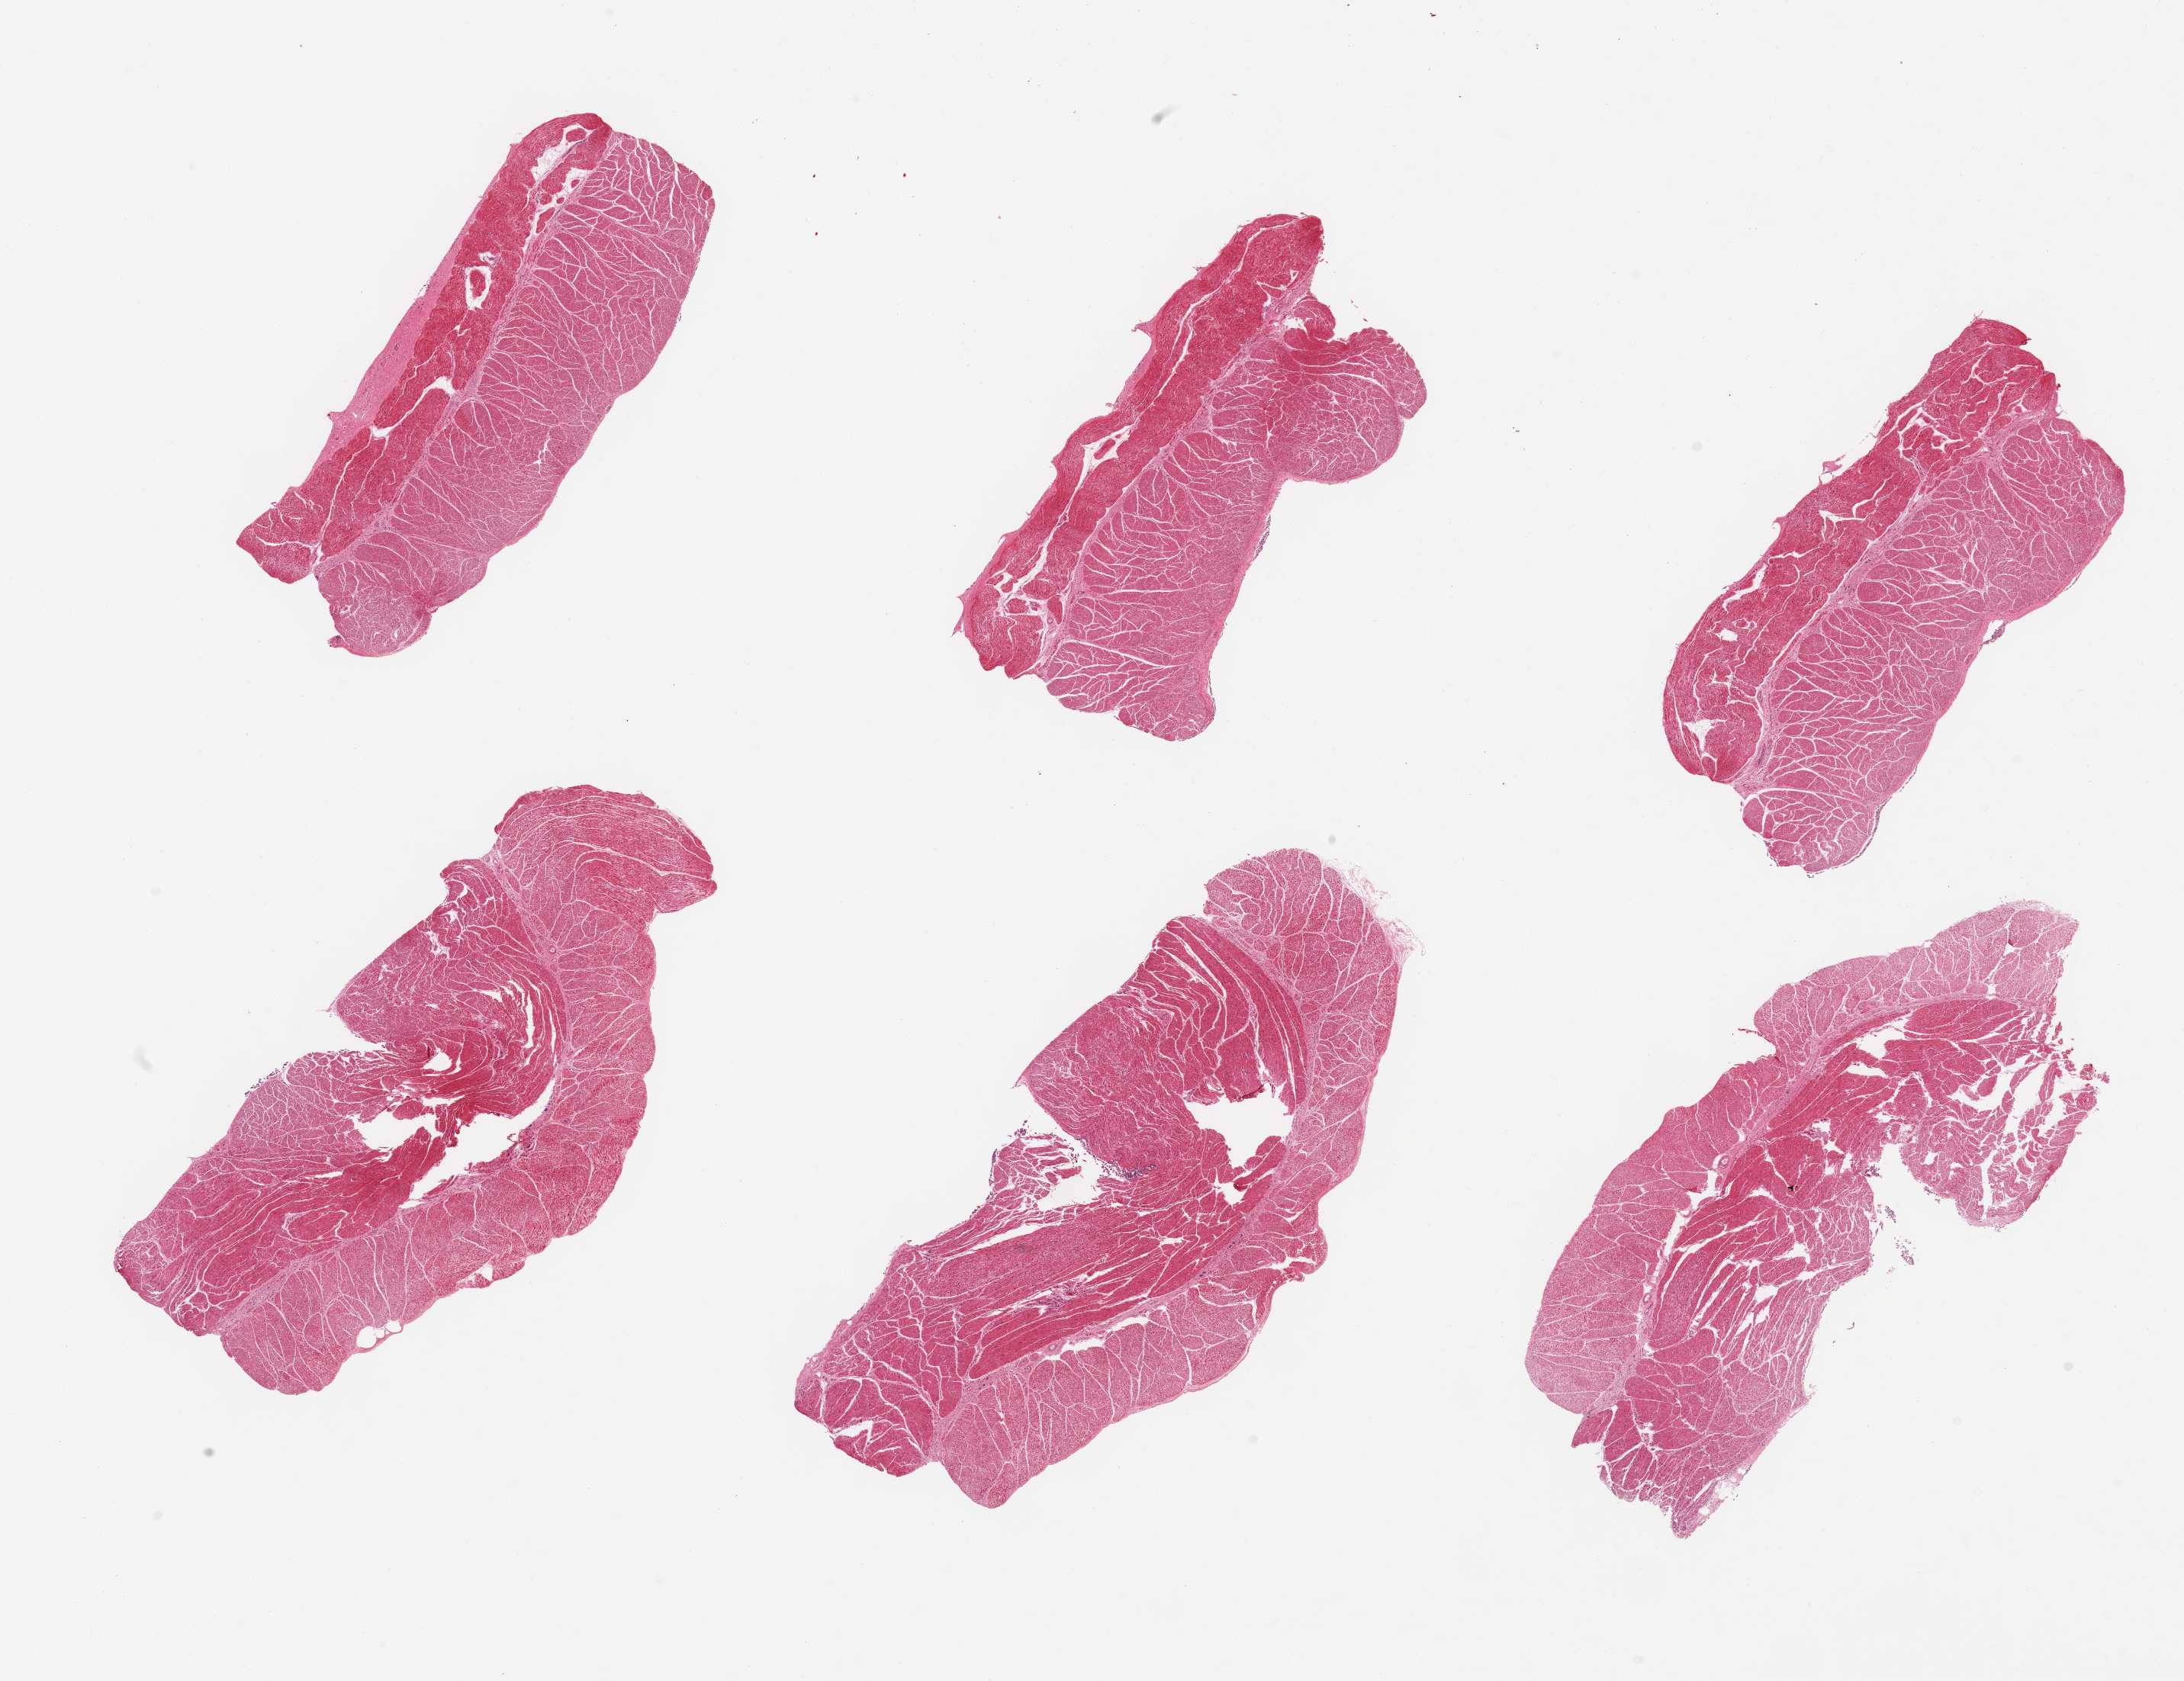
Digitized hematoxylin and eosin (H&E)-stained section, low-resolution overview of the scanned area, about 22.6 x 17.4 mm (slide scanned at 20x). PAXgene-fixed, paraffin-embedded tissue. Sampled site (target tissue): esophageal muscle. Tissue donor sample. Donor sex: male.
- reviewer comment on this tissue sample: 6 pieces; small surface deposits of sloughed squamous epithelial cells on all pieces (carry-over), otherwise well trimmed muscle